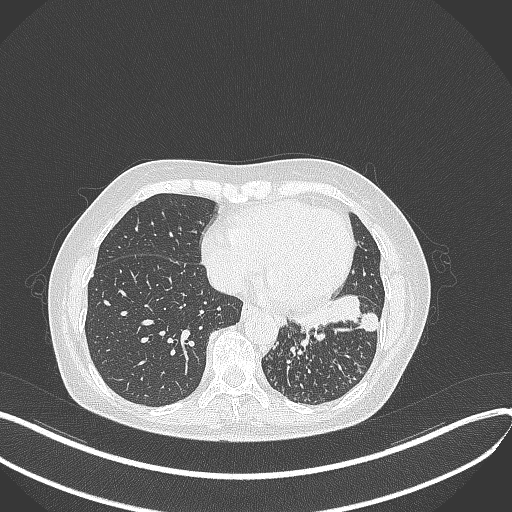
Chest CT, one axial slice; slice 139 of 429 in the series (ordered by position); reconstruction kernel B70f; 100 kVp; lung window (W 1500 / L -600 HU); 512 × 512 image matrix, field of view 400 × 400 mm. Patient: female, 63 years. From the clinical record (not read from this slice): clinical TNM (as recorded): T1b N0 M0; histopathological grade: G2-3.
Annotated regions visible in this slice (rectangle marked by the reading radiologist):
- lung tumour (recorded histology: adenocarcinoma): bounding box <290,289,378,341> (left, top, right, bottom; pixels)